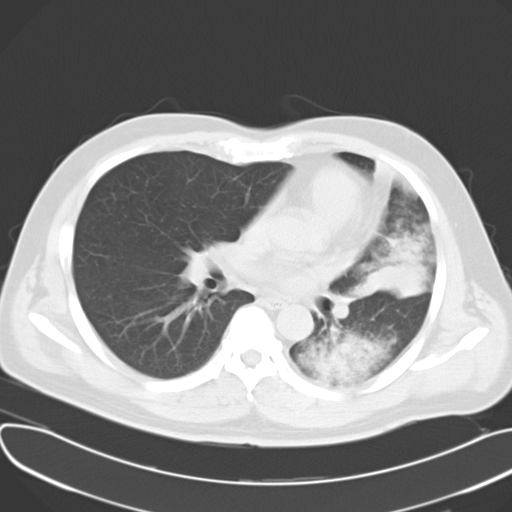
Chest CT, one axial slice. Position 17 of 30 along the scan axis. Reconstruction kernel B40f. 120 kVp. Lung window (W 1500 / L -600 HU). 10 mm slice thickness. 512 × 512 image matrix, field of view 377 × 377 mm. Male patient, age 48 years. From the clinical record (not read from this slice): clinical TNM (as recorded): T4 N0 M0.
Outlined on this slice (rectangle marked by the reading radiologist):
- lung tumour (recorded histology: adenocarcinoma): box from (x=353, y=228) to (x=428, y=308) px